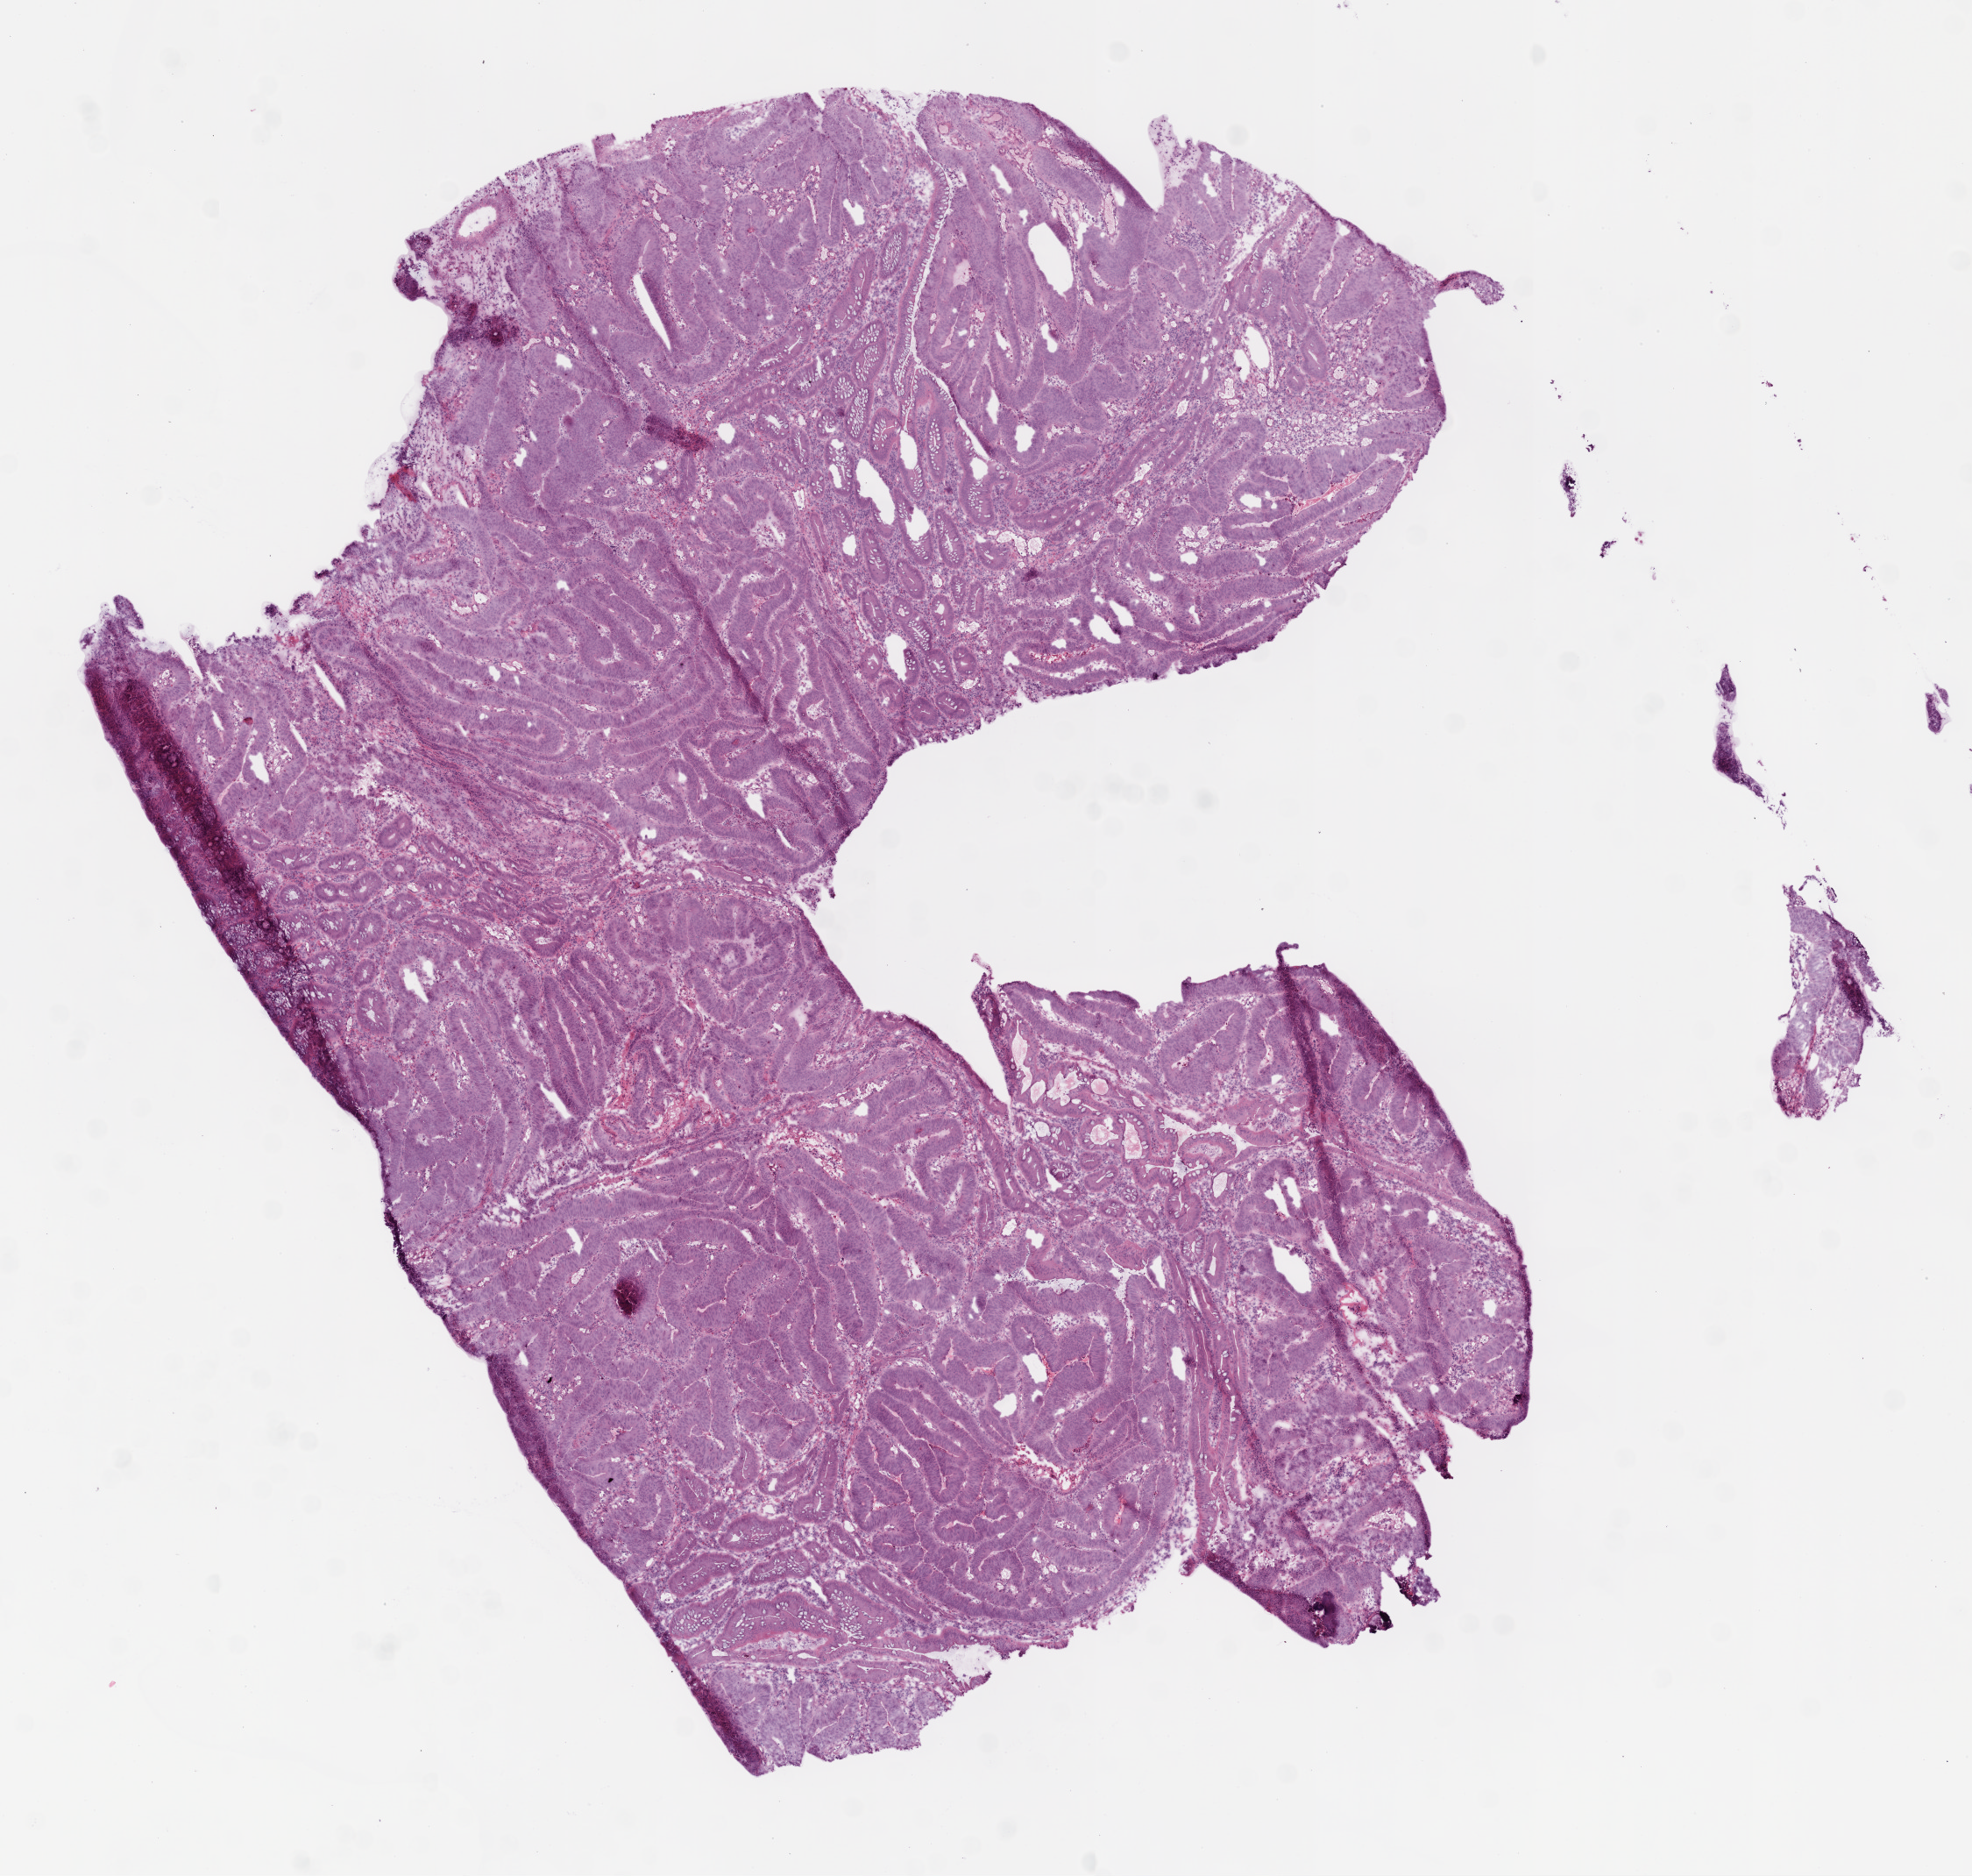
Digitized H&E tissue section (whole slide) — shown as a low-resolution overview of the whole scanned area (about 9.0 x 8.6 mm, acquisition: 20x scan), frozen section from the top of the tissue portion, primary tumour sample from the colon. Female, age 60 years at initial diagnosis. Pathologist review of this section (percent, as recorded): tumour cells 90%, tumour nuclei 90%, normal cells 5%, stromal cells 5%, necrosis 0%.
• AJCC pathologic stage: III (5th edition)
• histologic diagnosis: Adenocarcinoma, NOS (sigmoid colon)